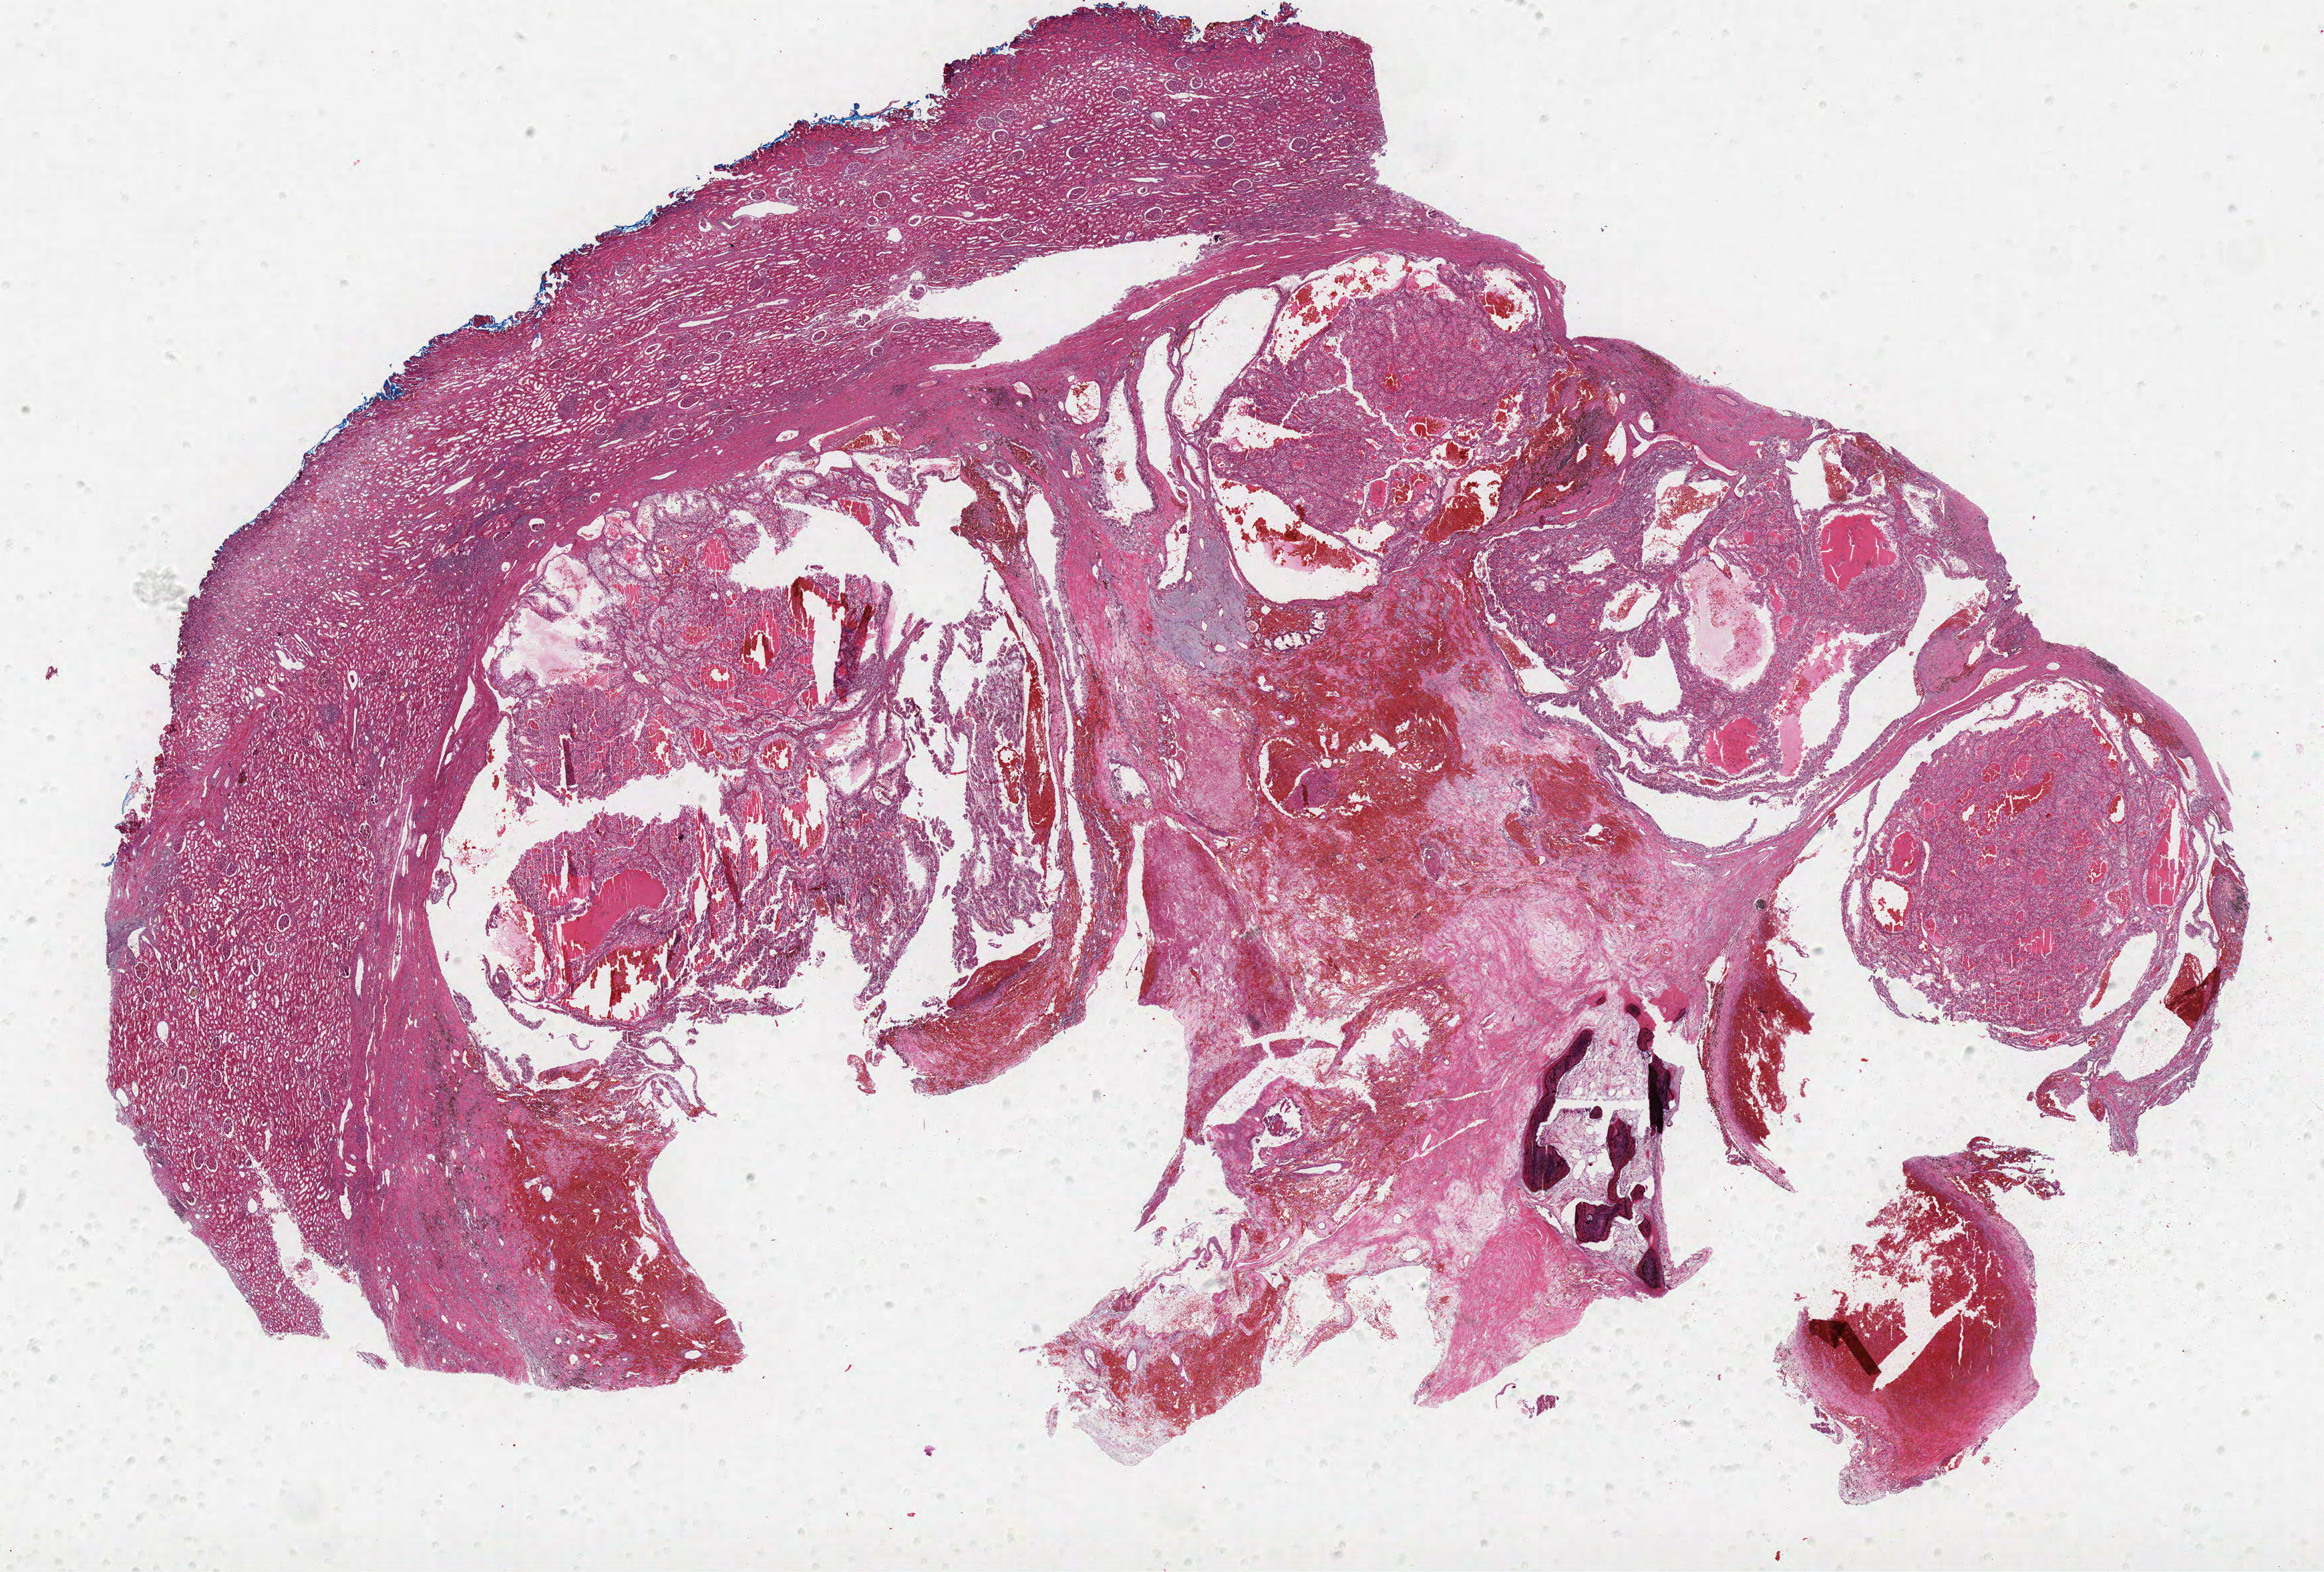
Hematoxylin and eosin (H&E) stained whole-slide image, whole scanned area (about 27.8 x 18.8 mm, acquisition: 40x scan) shown as a low-resolution overview; formalin-fixed paraffin-embedded (FFPE) diagnostic section; sample: primary tumour, kidney. Male patient; age at initial diagnosis 56 years. Histologic grade: G3 (poorly differentiated).
Lymph nodes positive (case pathology): 0 of 1 examined. Histologic diagnosis: Clear cell adenocarcinoma, NOS. AJCC pathologic stage: I. TNM: T1a N0 M0.